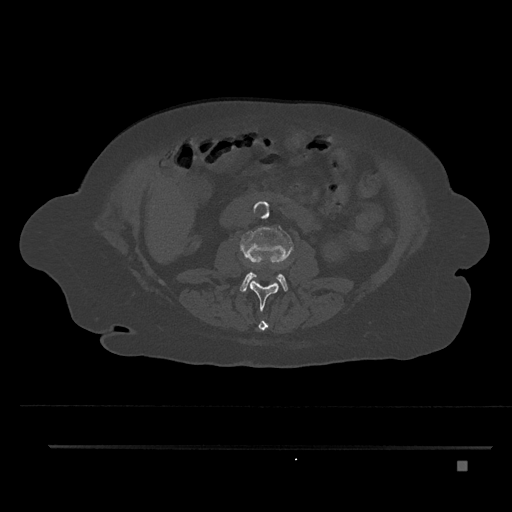
CT including the spine, one axial slice; 120 kVp; bone window (W 1800 / L 400 HU); 512 × 512 image matrix, field of view 437 × 437 mm. Female patient, age 76 years. From the clinical record (not read from this slice): primary cancer: lung.
Structures marked on this image (semi-automatic segmentation, software-assisted and operator-edited):
- L1 vertebra: bounding box [x1, y1, x2, y2] px = [258, 320, 268, 331]
- L2 vertebra: [249, 263, 279, 311]
- L3 vertebra: [240, 225, 293, 292]